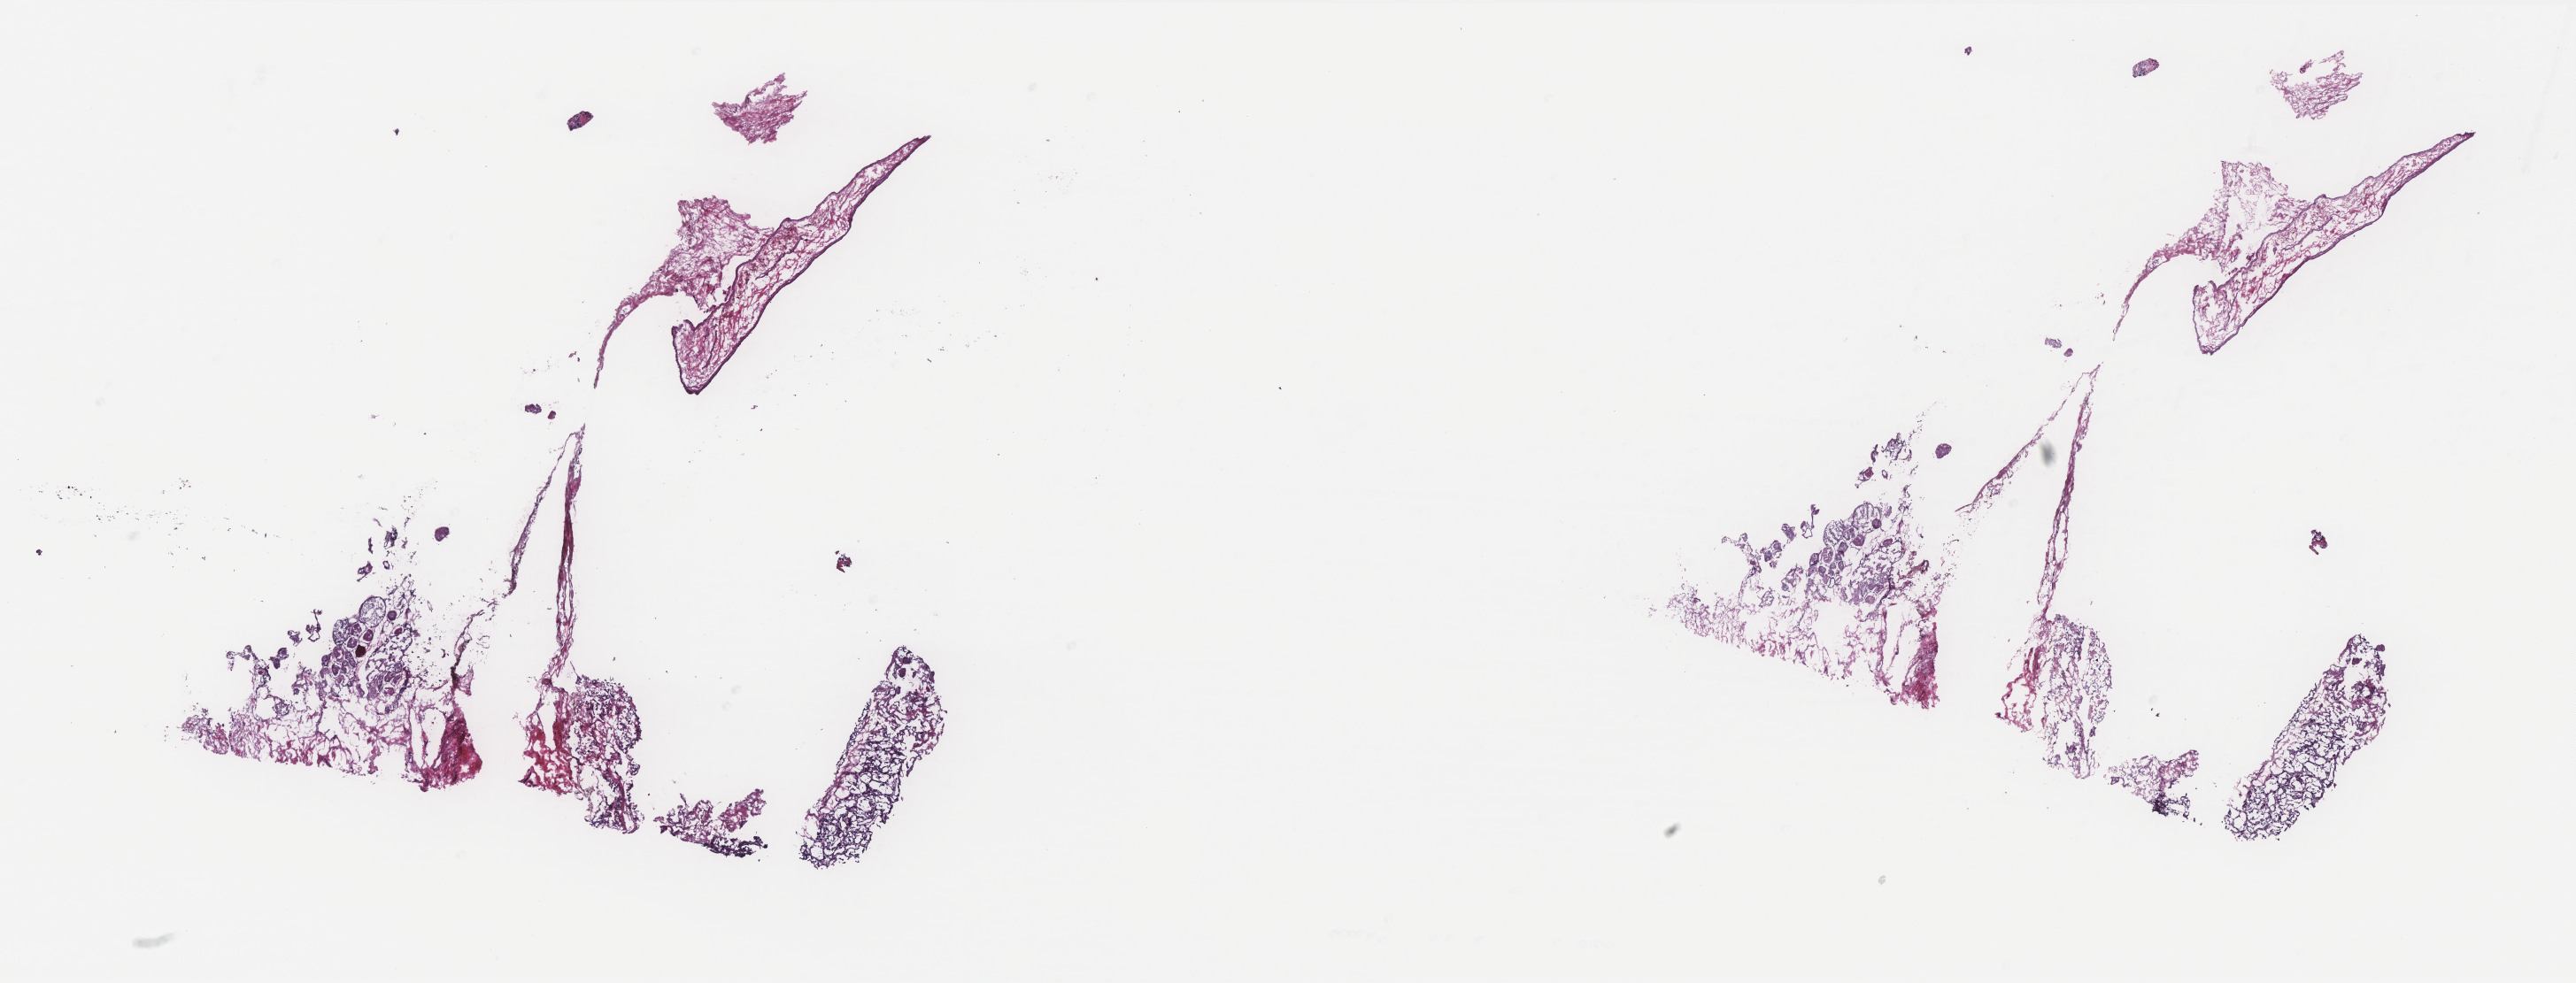
Hematoxylin and eosin (H&E) stained whole-slide image — whole scanned area (about 23.3 x 8.9 mm) shown as a low-resolution overview. Frozen section from the bottom of the tissue portion. Thyroid, primary tumour sample. Male patient; age at initial diagnosis 80 years. Slide review estimates, as recorded: tumour cells 70%, tumour nuclei 99%, normal cells 0%, stromal cells 30%, necrosis 0%. Infiltration values recorded for this section: lymphocyte infiltration 0%, monocyte infiltration 0%, neutrophil infiltration 0%.
- histologic diagnosis: Papillary carcinoma, follicular variant (thyroid gland)
- TNM: T1 N0 M0
- AJCC pathologic stage: I (7th edition)